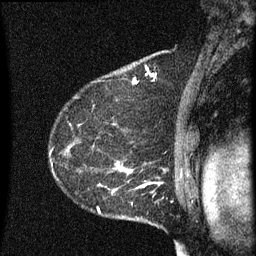
Breast MRI (dynamic contrast-enhanced), one sagittal slice; dynamic contrast-enhanced series, image 2 of 3 at this slice position (ordered by acquisition); 1.5 T; TE 4.2 ms, TR 8 ms; 2 mm slice thickness; 256 × 256 image matrix. Female patient, age 55 years.
Annotated regions visible in this slice (semi-automatically segmented with operator editing):
- analysis volume of interest (the breast-tissue region the enhancement analysis was run in; not a lesion): bounding box (x1, y1, x2, y2) in pixels: (51, 156, 145, 217)
- tumour enhancement mask (voxels above the 70 % enhancement threshold inside the analysis volume of interest): (98, 162, 145, 213)